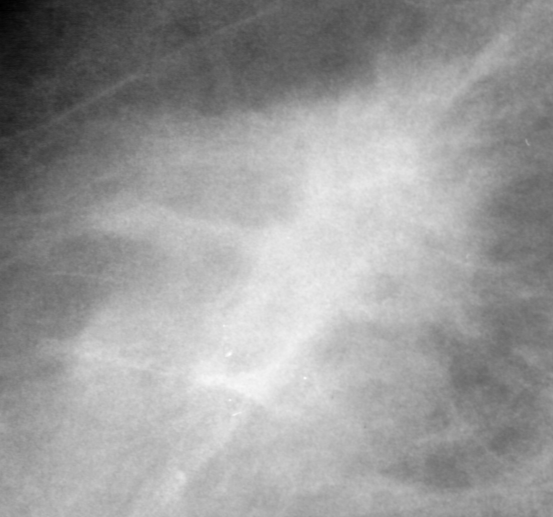
Cropped region of a digitized screen-film mammogram centred on a radiologist-marked abnormality; right breast; CC view.
Mass, shape irregular, margins spiculated; BI-RADS assessment category 0; subtlety rating 4 on a 1 (subtle) to 5 (obvious) scale; pathology (as recorded): malignant.